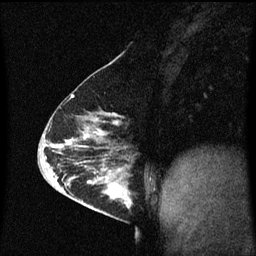
Breast MRI (dynamic contrast-enhanced), one sagittal slice; slice 29 of 60 in the series (ordered by position); dynamic contrast-enhanced series, image 2 of 3 at this slice position (ordered by acquisition); 1.5 T; TE 4.2 ms, TR 8.4 ms; 256 × 256 image matrix, field of view 200 × 200 mm. Female patient, age 63 years.
Outlined on this slice (semi-automatic segmentation, software-assisted and operator-edited):
- analysis volume of interest (the breast-tissue region the enhancement analysis was run in; not a lesion): box from (x=98, y=168) to (x=137, y=217) px
- tumour enhancement mask (voxels above the 70 % enhancement threshold inside the analysis volume of interest): (x=98, y=168)–(x=131, y=209)